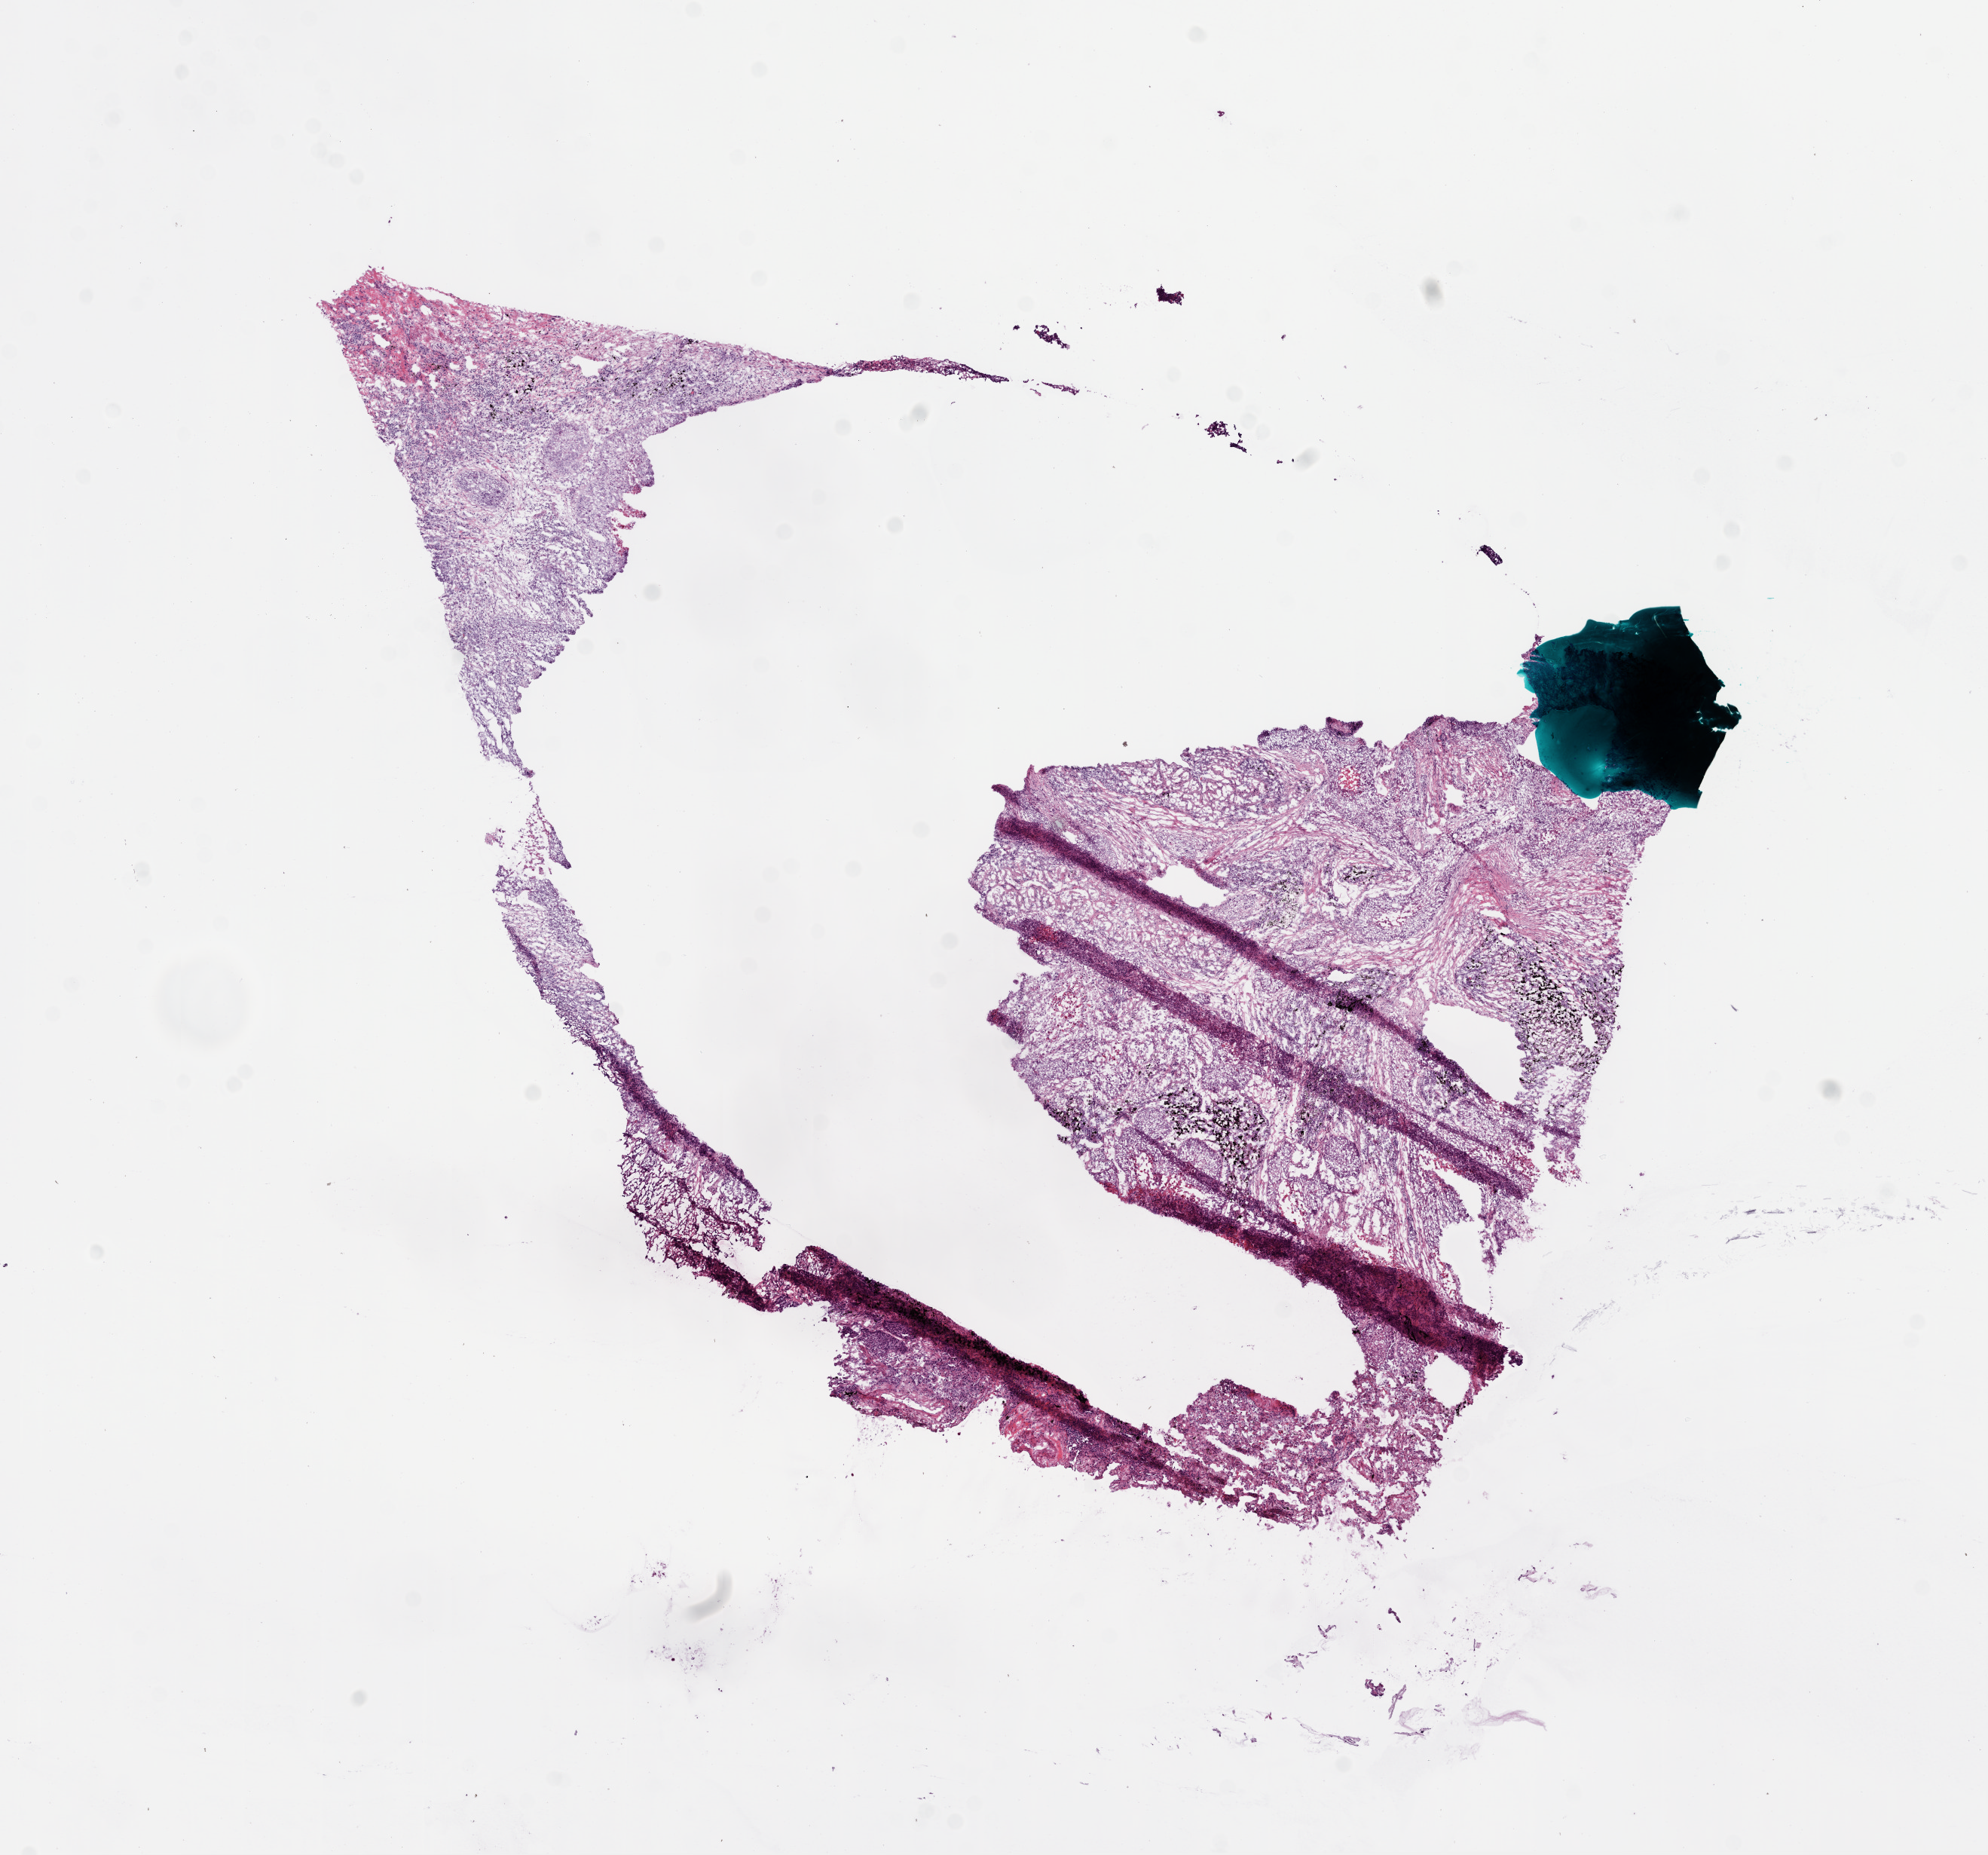
Whole-slide histology image, Hematoxylin and eosin (H&E) stained, whole scanned area (about 10.6 x 9.9 mm) shown as a low-resolution overview, frozen section from the bottom of the tissue portion, lung, primary tumour sample. Male, age 64 years at initial diagnosis. Composition of this section per pathologist review: tumour nuclei 80%, necrosis 0%.
Histologic diagnosis: Squamous cell carcinoma, NOS (upper lobe, lung).